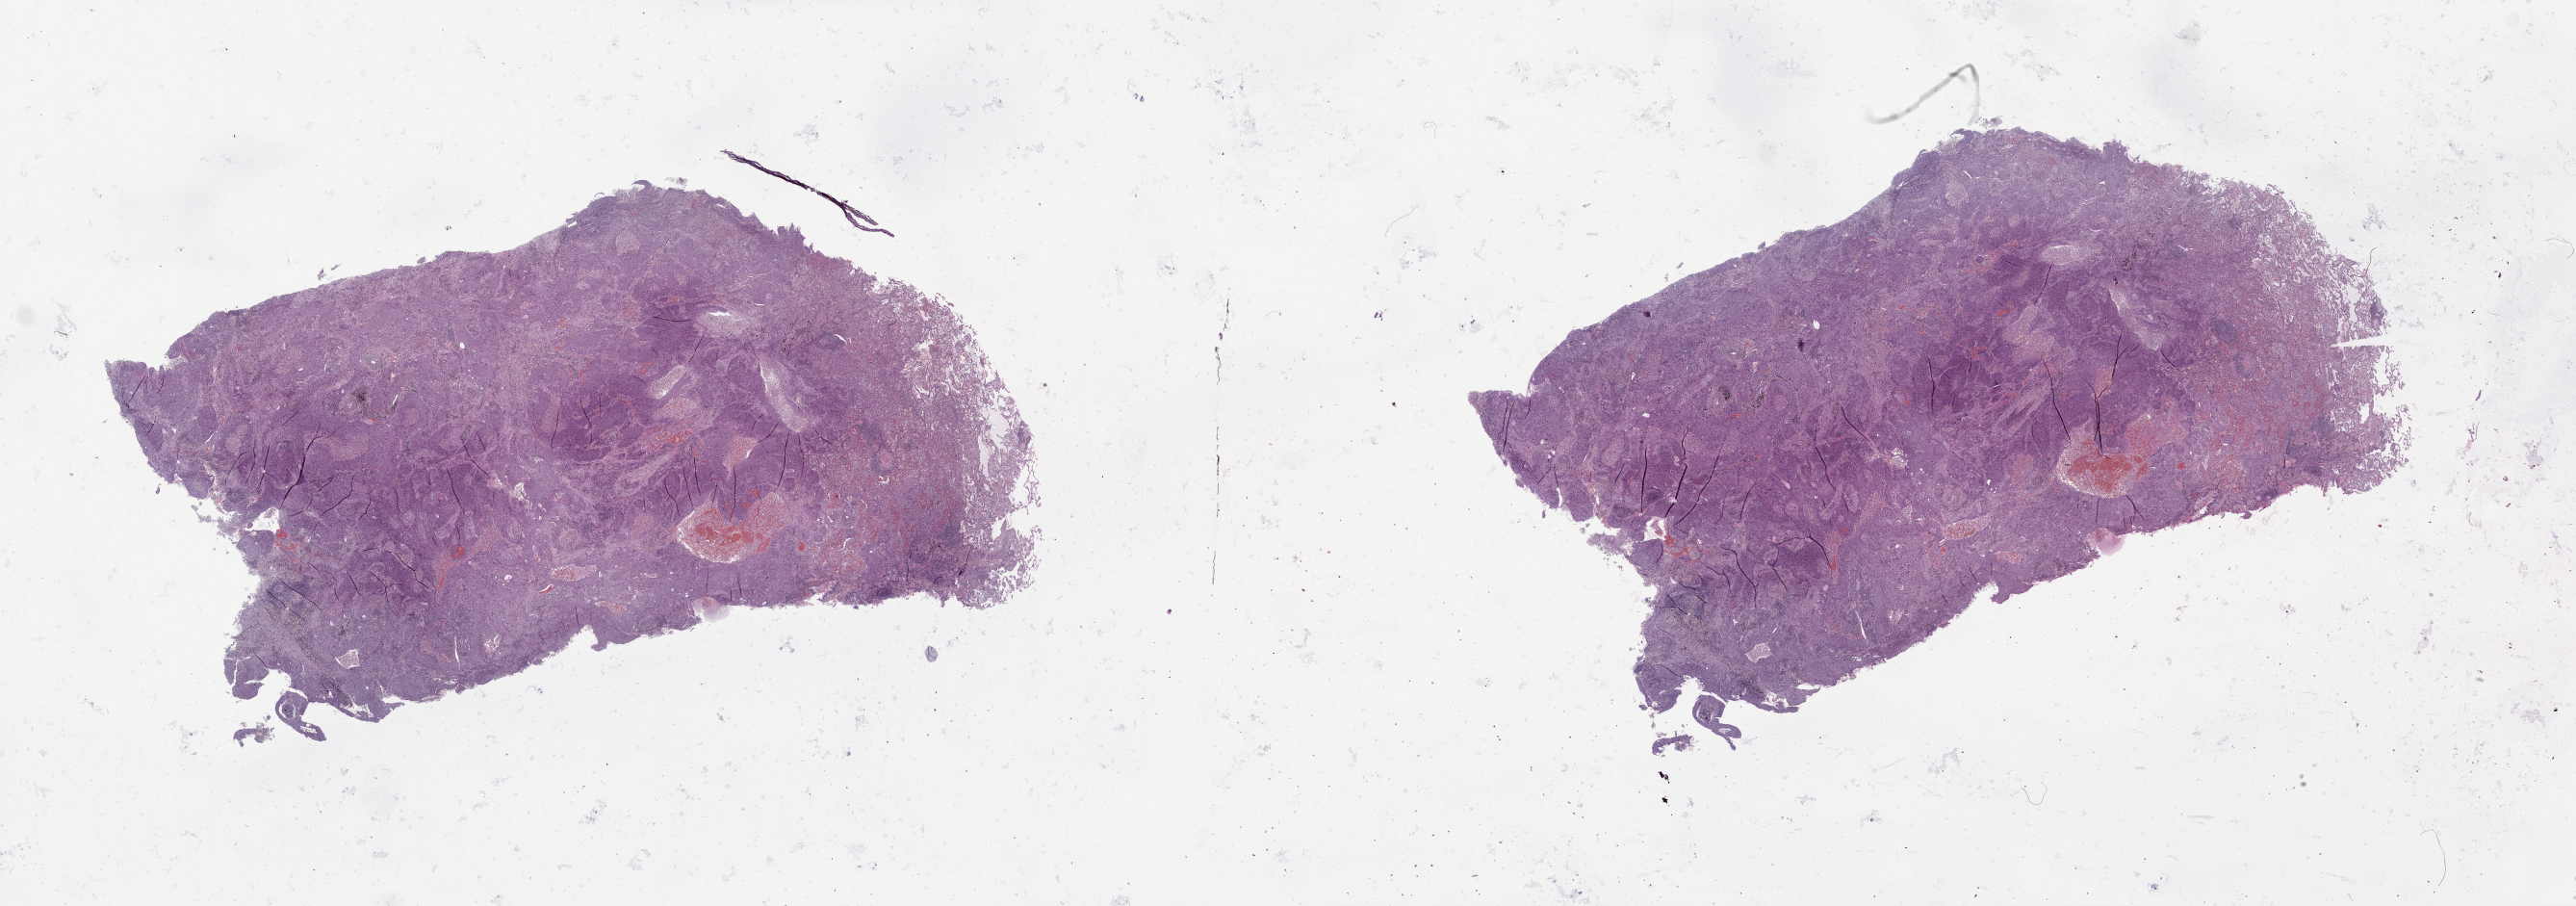
Whole-slide histology image, H&E-stained — shown as a low-resolution overview of the whole scanned area (about 43.1 x 15.2 mm). Lung, tumour tissue. 75-year-old male patient.
Patient diagnosis (cohort enrolment): squamous cell carcinoma (lung).